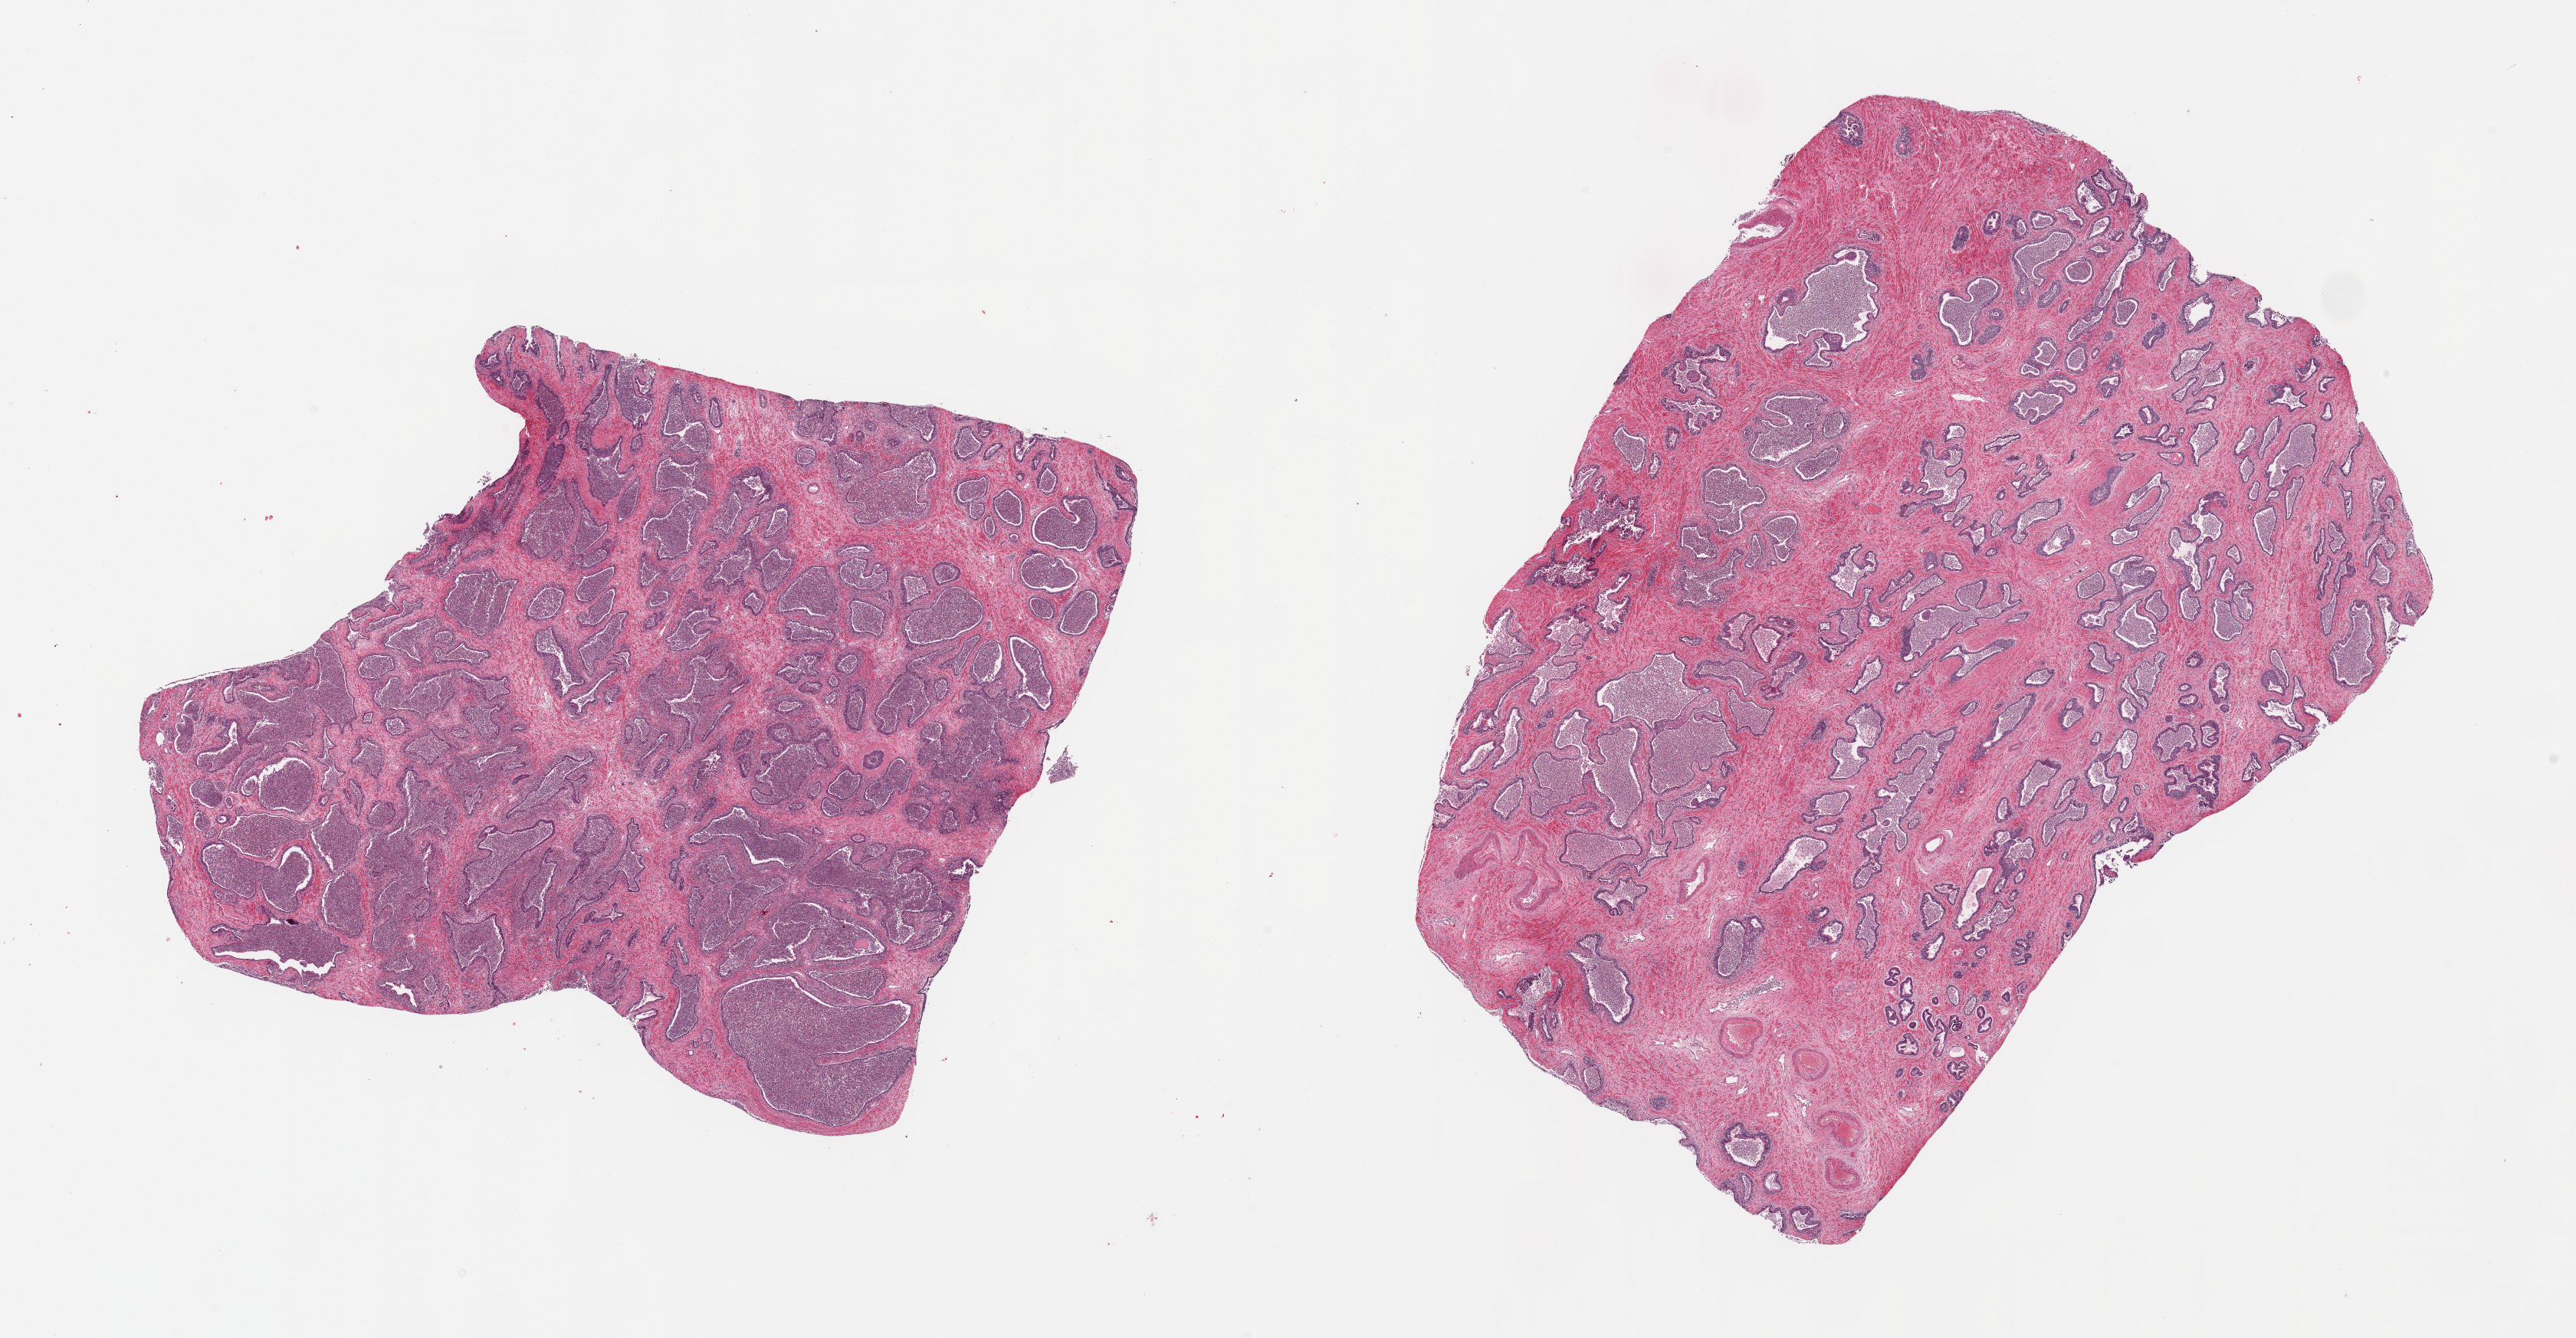
Whole-slide image, hematoxylin and eosin (H&E) stain — a low-resolution overview of the entire scanned area, about 26.6 x 13.8 mm (acquisition: 20x scan), PAXgene-fixed paraffin-embedded (PFPE) section, section of prostate (target tissue), donor tissue sample.
* pathologist's review note for this sample: 2 pieces, diffuse suppurative/acute prostatitis